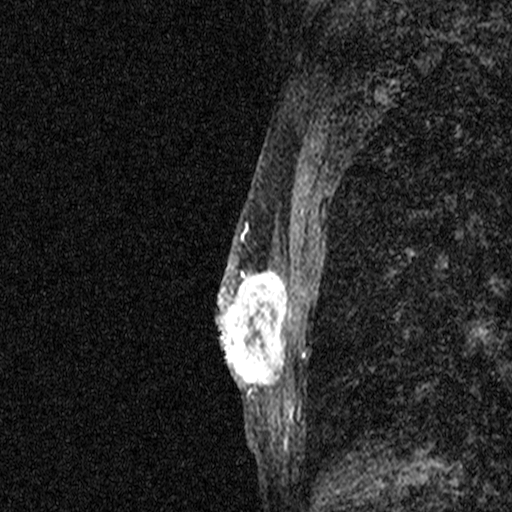
Breast MRI (dynamic contrast-enhanced), one sagittal slice. Slice 27 of 44 in the series (ordered by position). Dynamic contrast-enhanced study with each time point stored as its own series, time point 2 of 3 at this slice position (early post-contrast, ordered by acquisition time). 1.5 T. TE 4.5 ms, TR 11 ms. 2.05 mm slice thickness. 512 × 512 image matrix. Patient: female, 44 years. Case-level facts recorded for this patient, not image findings: setting: breast cancer imaged before/during neoadjuvant chemotherapy; receptor status: HR-positive, HER2-negative.
Outlined on this slice (semi-automatic segmentation, software-assisted and operator-edited):
- analysis volume of interest (the breast-tissue region the enhancement analysis was run in; not a lesion): bounding box (x1, y1, x2, y2) in pixels: (204, 254, 289, 401)
- tumour enhancement mask (voxels above the 90 % enhancement threshold inside the analysis volume of interest): (218, 256, 286, 399)